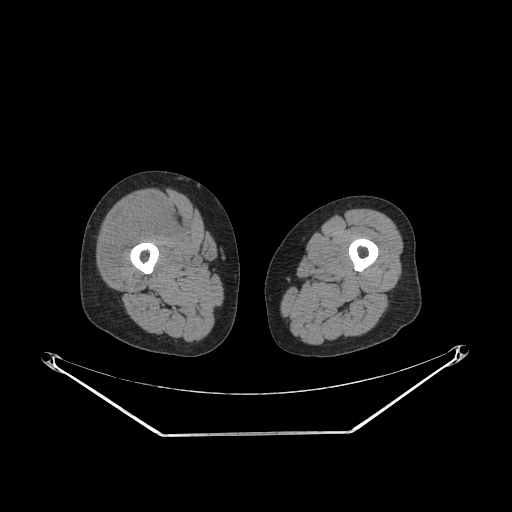
CT of an extremity soft-tissue mass (from a PET/CT study), one axial slice; slice 229 of 311 in the series (ordered by position); reconstruction kernel SOFT; 140 kVp; soft-tissue window (W 400 / L 40 HU); 3.75 mm slice thickness; 512 × 512 image matrix, field of view 500 × 500 mm. Female patient. Case-level facts recorded for this patient, not image findings: histological type: pleiomorphic undifferentiated sarcoma; grade: high; site of the primary tumour: right quadricep.
Annotated regions visible in this slice (expert contour drawn on MRI and transferred to this co-registered scan by the dataset authors):
- tumour plus oedema (research contour): bounding box (x1, y1, x2, y2) in pixels: (103, 203, 179, 277)